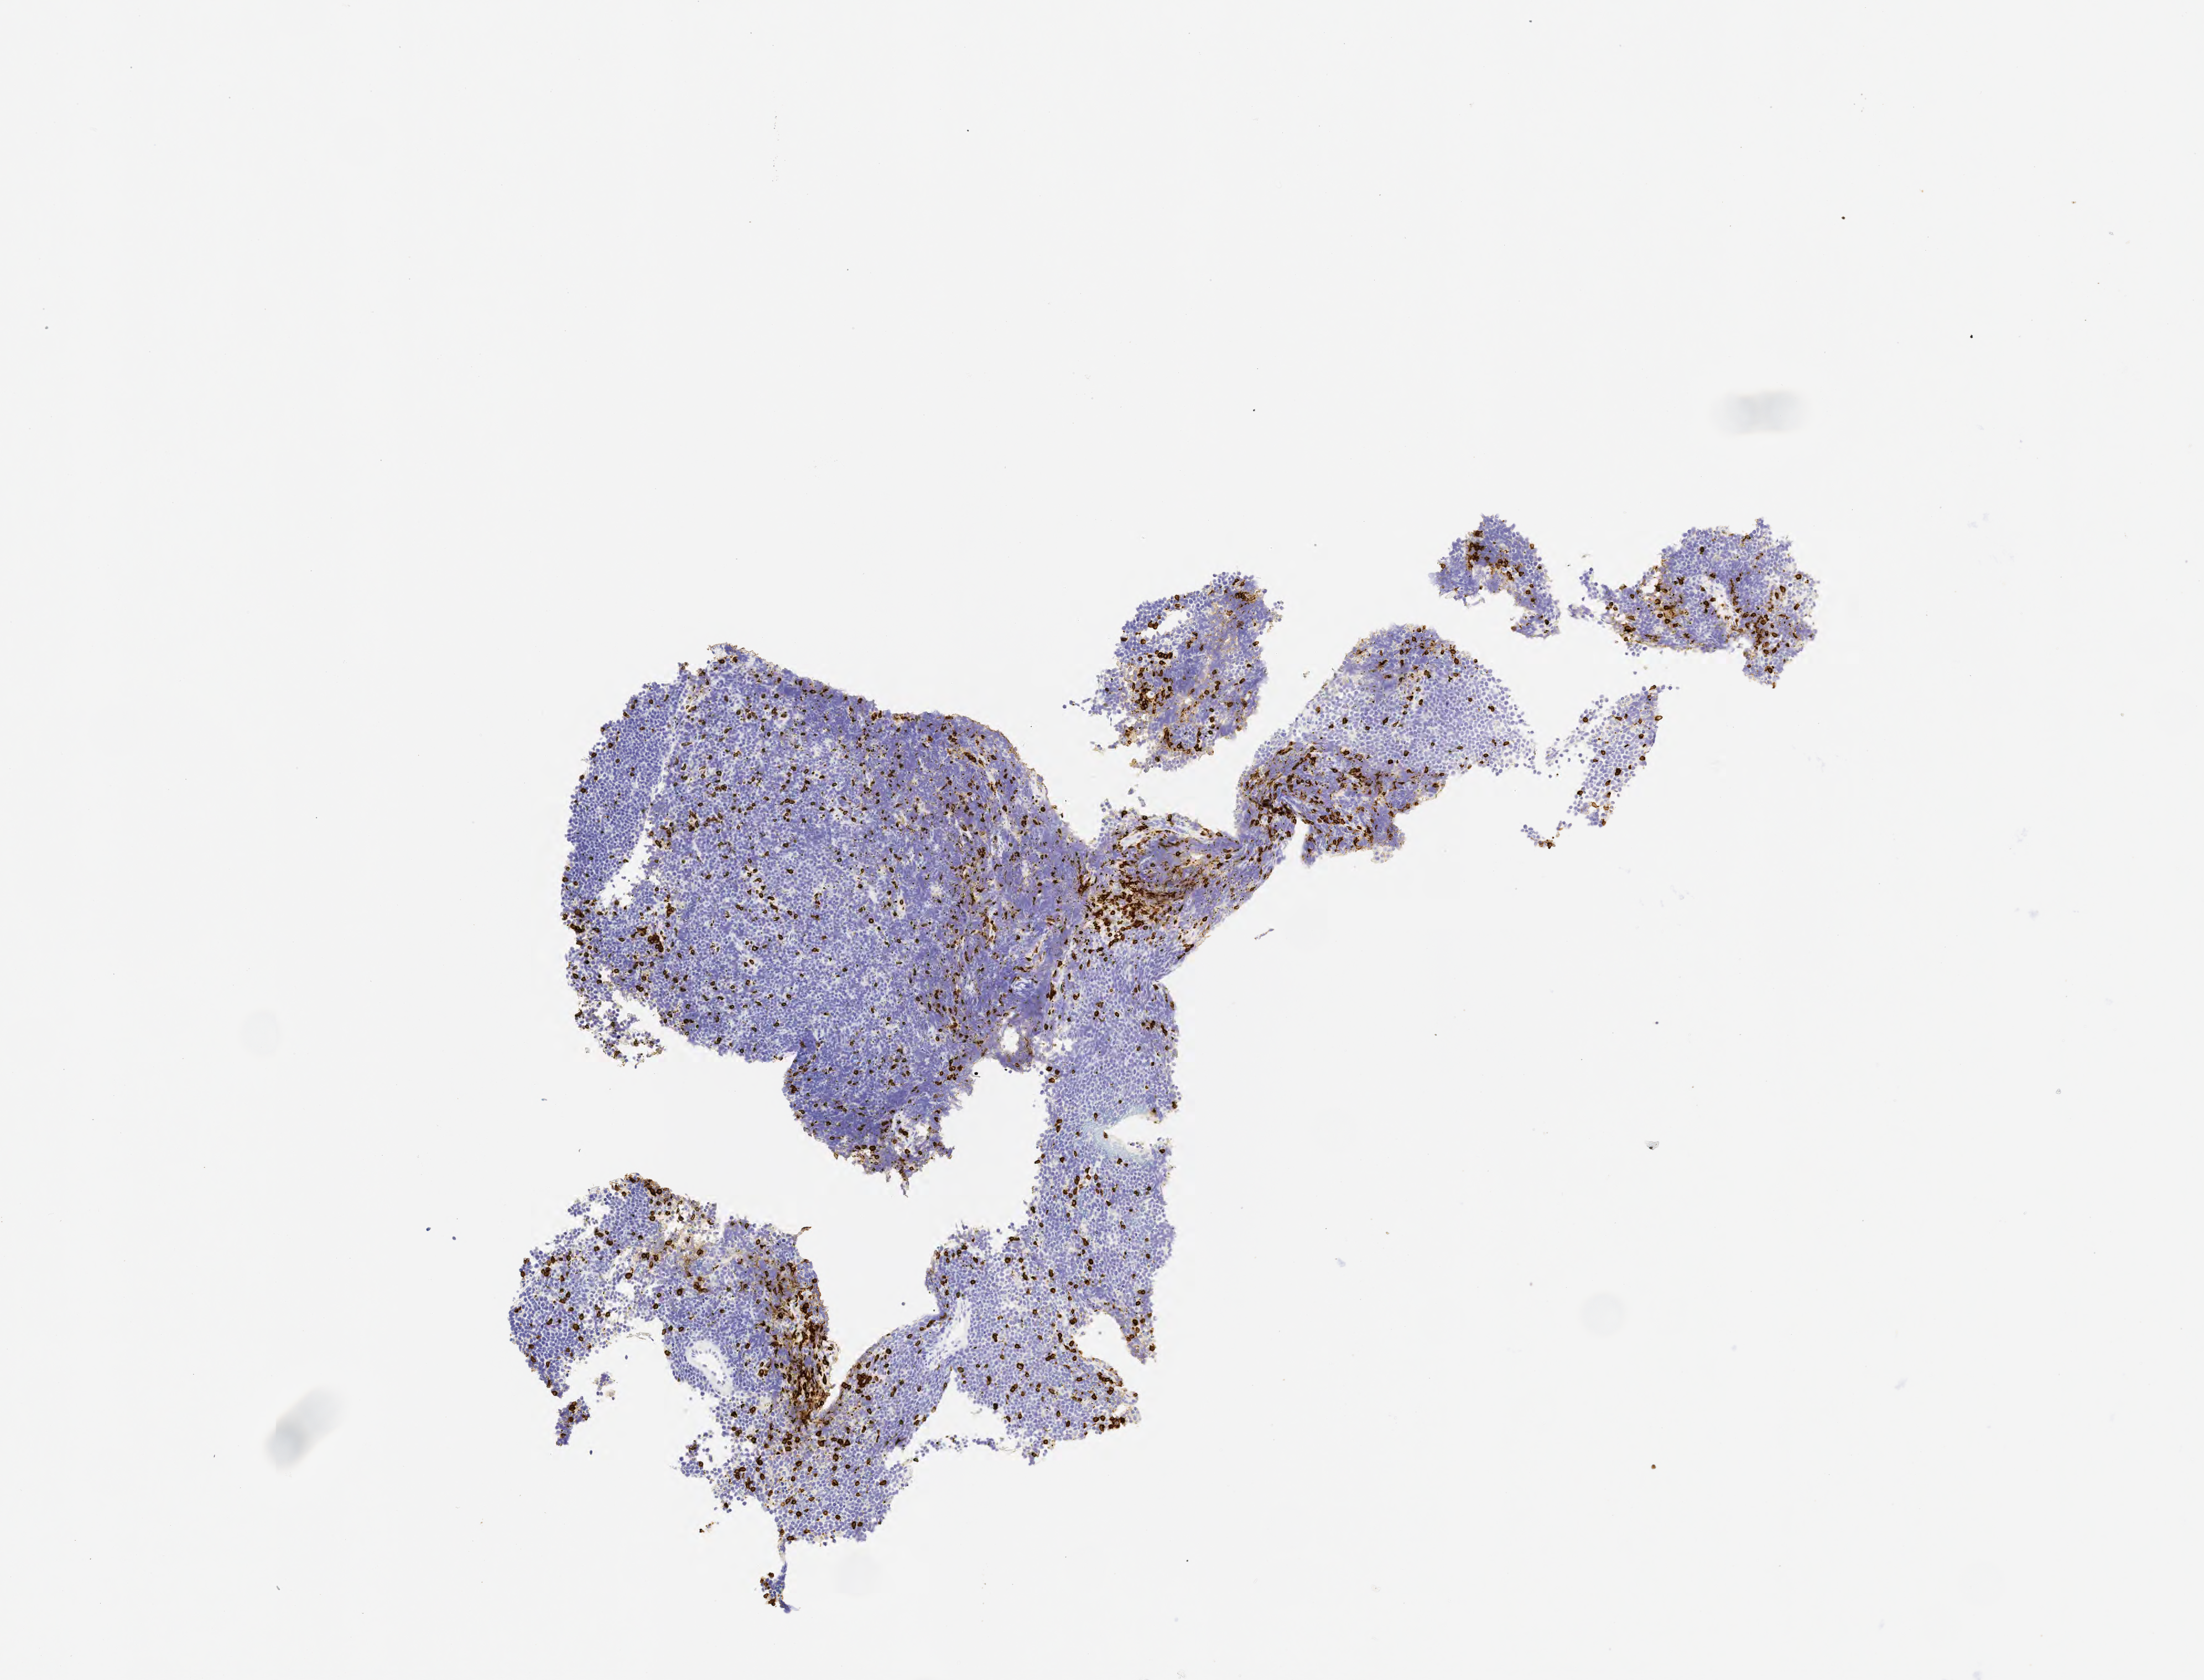
IHC for CD3, whole-slide image — low-resolution overview of the scanned area, about 4.0 x 3.1 mm; specimen: tumor tissue. Male, age 8 years at initial diagnosis.
- histologic diagnosis: Burkitt lymphoma, NOS